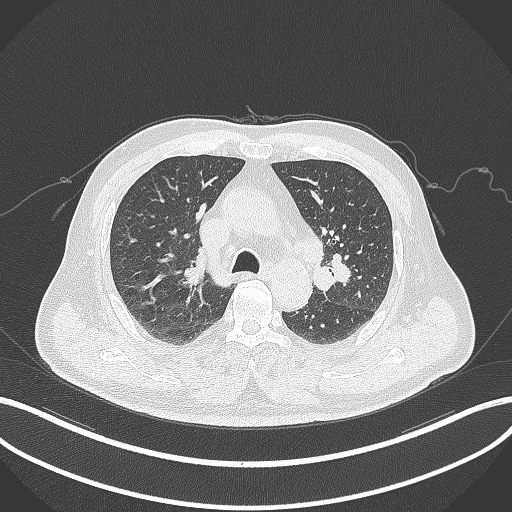
Chest CT, one axial slice. Slice 202 of 286 in the series (ordered by position). Reconstruction kernel B70f. 120 kVp. Lung window (W 1500 / L -600 HU). 1 mm slice thickness. 512 × 512 image matrix. Male patient, age 67 years. From the clinical record (not read from this slice): clinical TNM (as recorded): T2a N1 M0; histopathological grade: G3.
Outlined on this slice (bounding box drawn by a radiologist):
- lung tumour (recorded histology: adenocarcinoma): bounding box (x1, y1, x2, y2) in pixels: (309, 252, 354, 293)